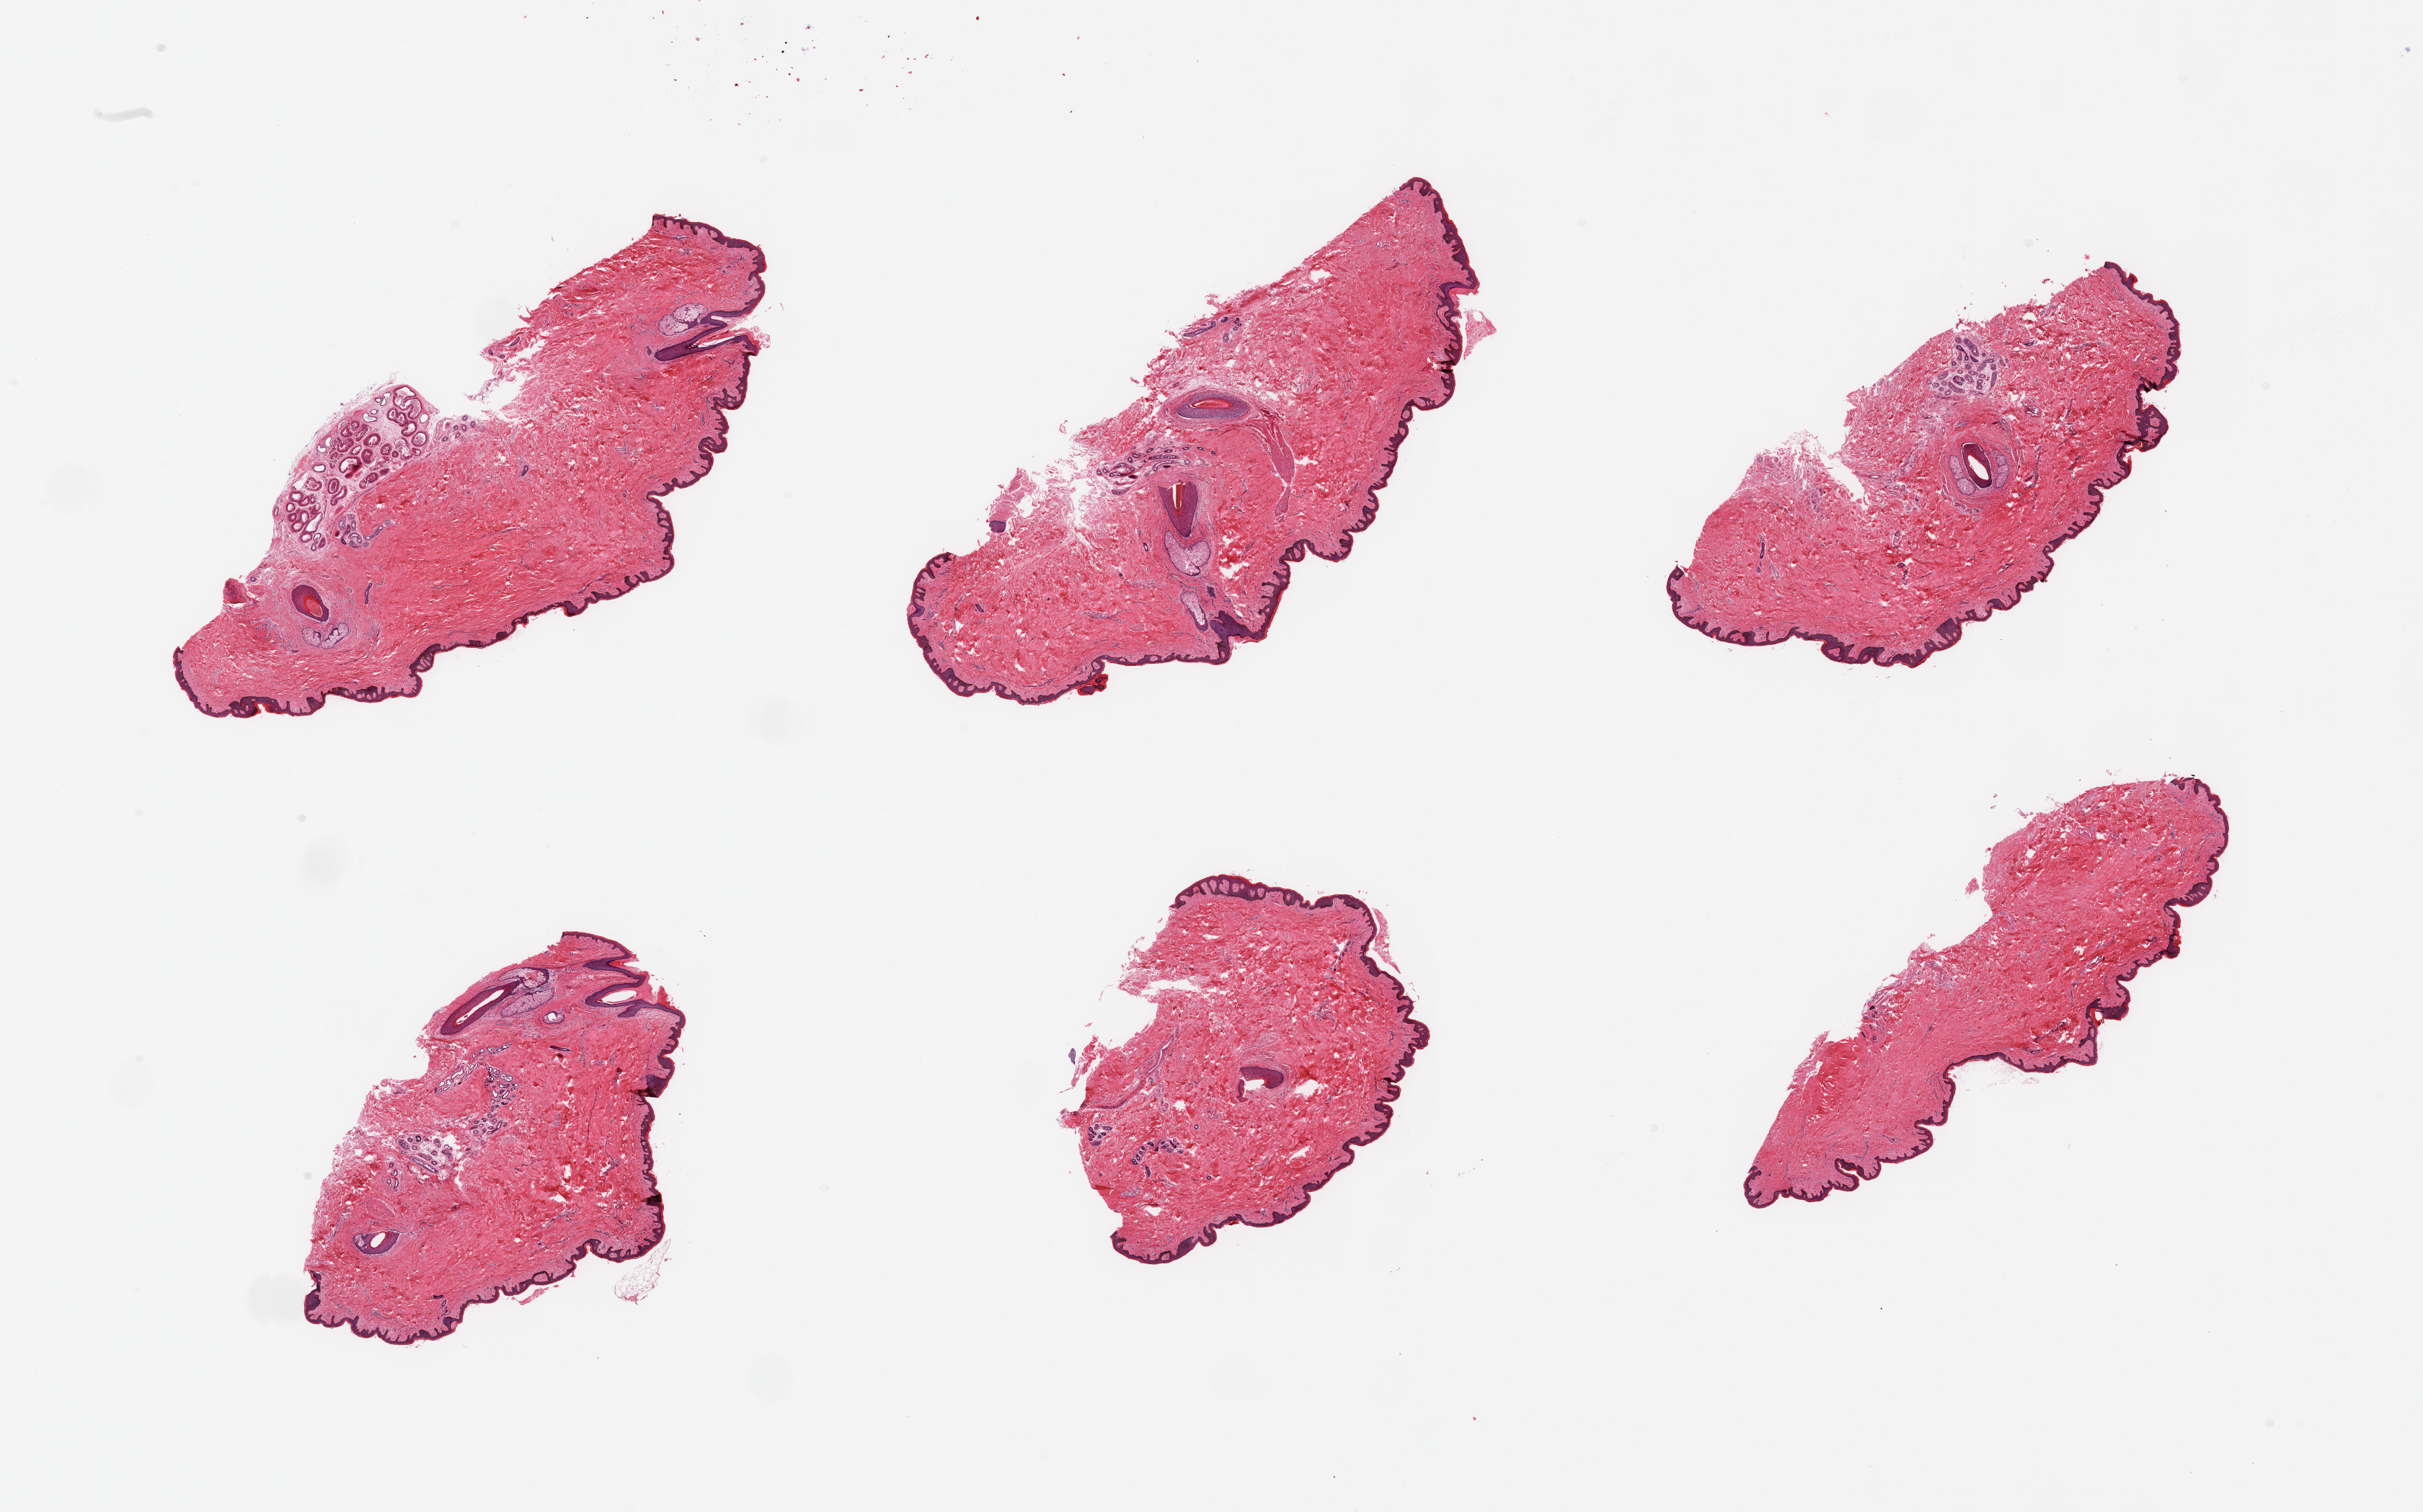
Digitized haematoxylin and eosin-stained section — whole scanned area (about 26.6 x 16.6 mm, from a 20x scan) shown as a low-resolution overview. PAXgene-fixed paraffin-embedded (PFPE) section. Section of skin of suprapubic region (target tissue). Donor tissue sample. Donor: male.
Pathologist's review note for this sample: 6 pieces; well trimmed; minimal dermal fat; 2 mm deep apocrine gland in 1 piece.